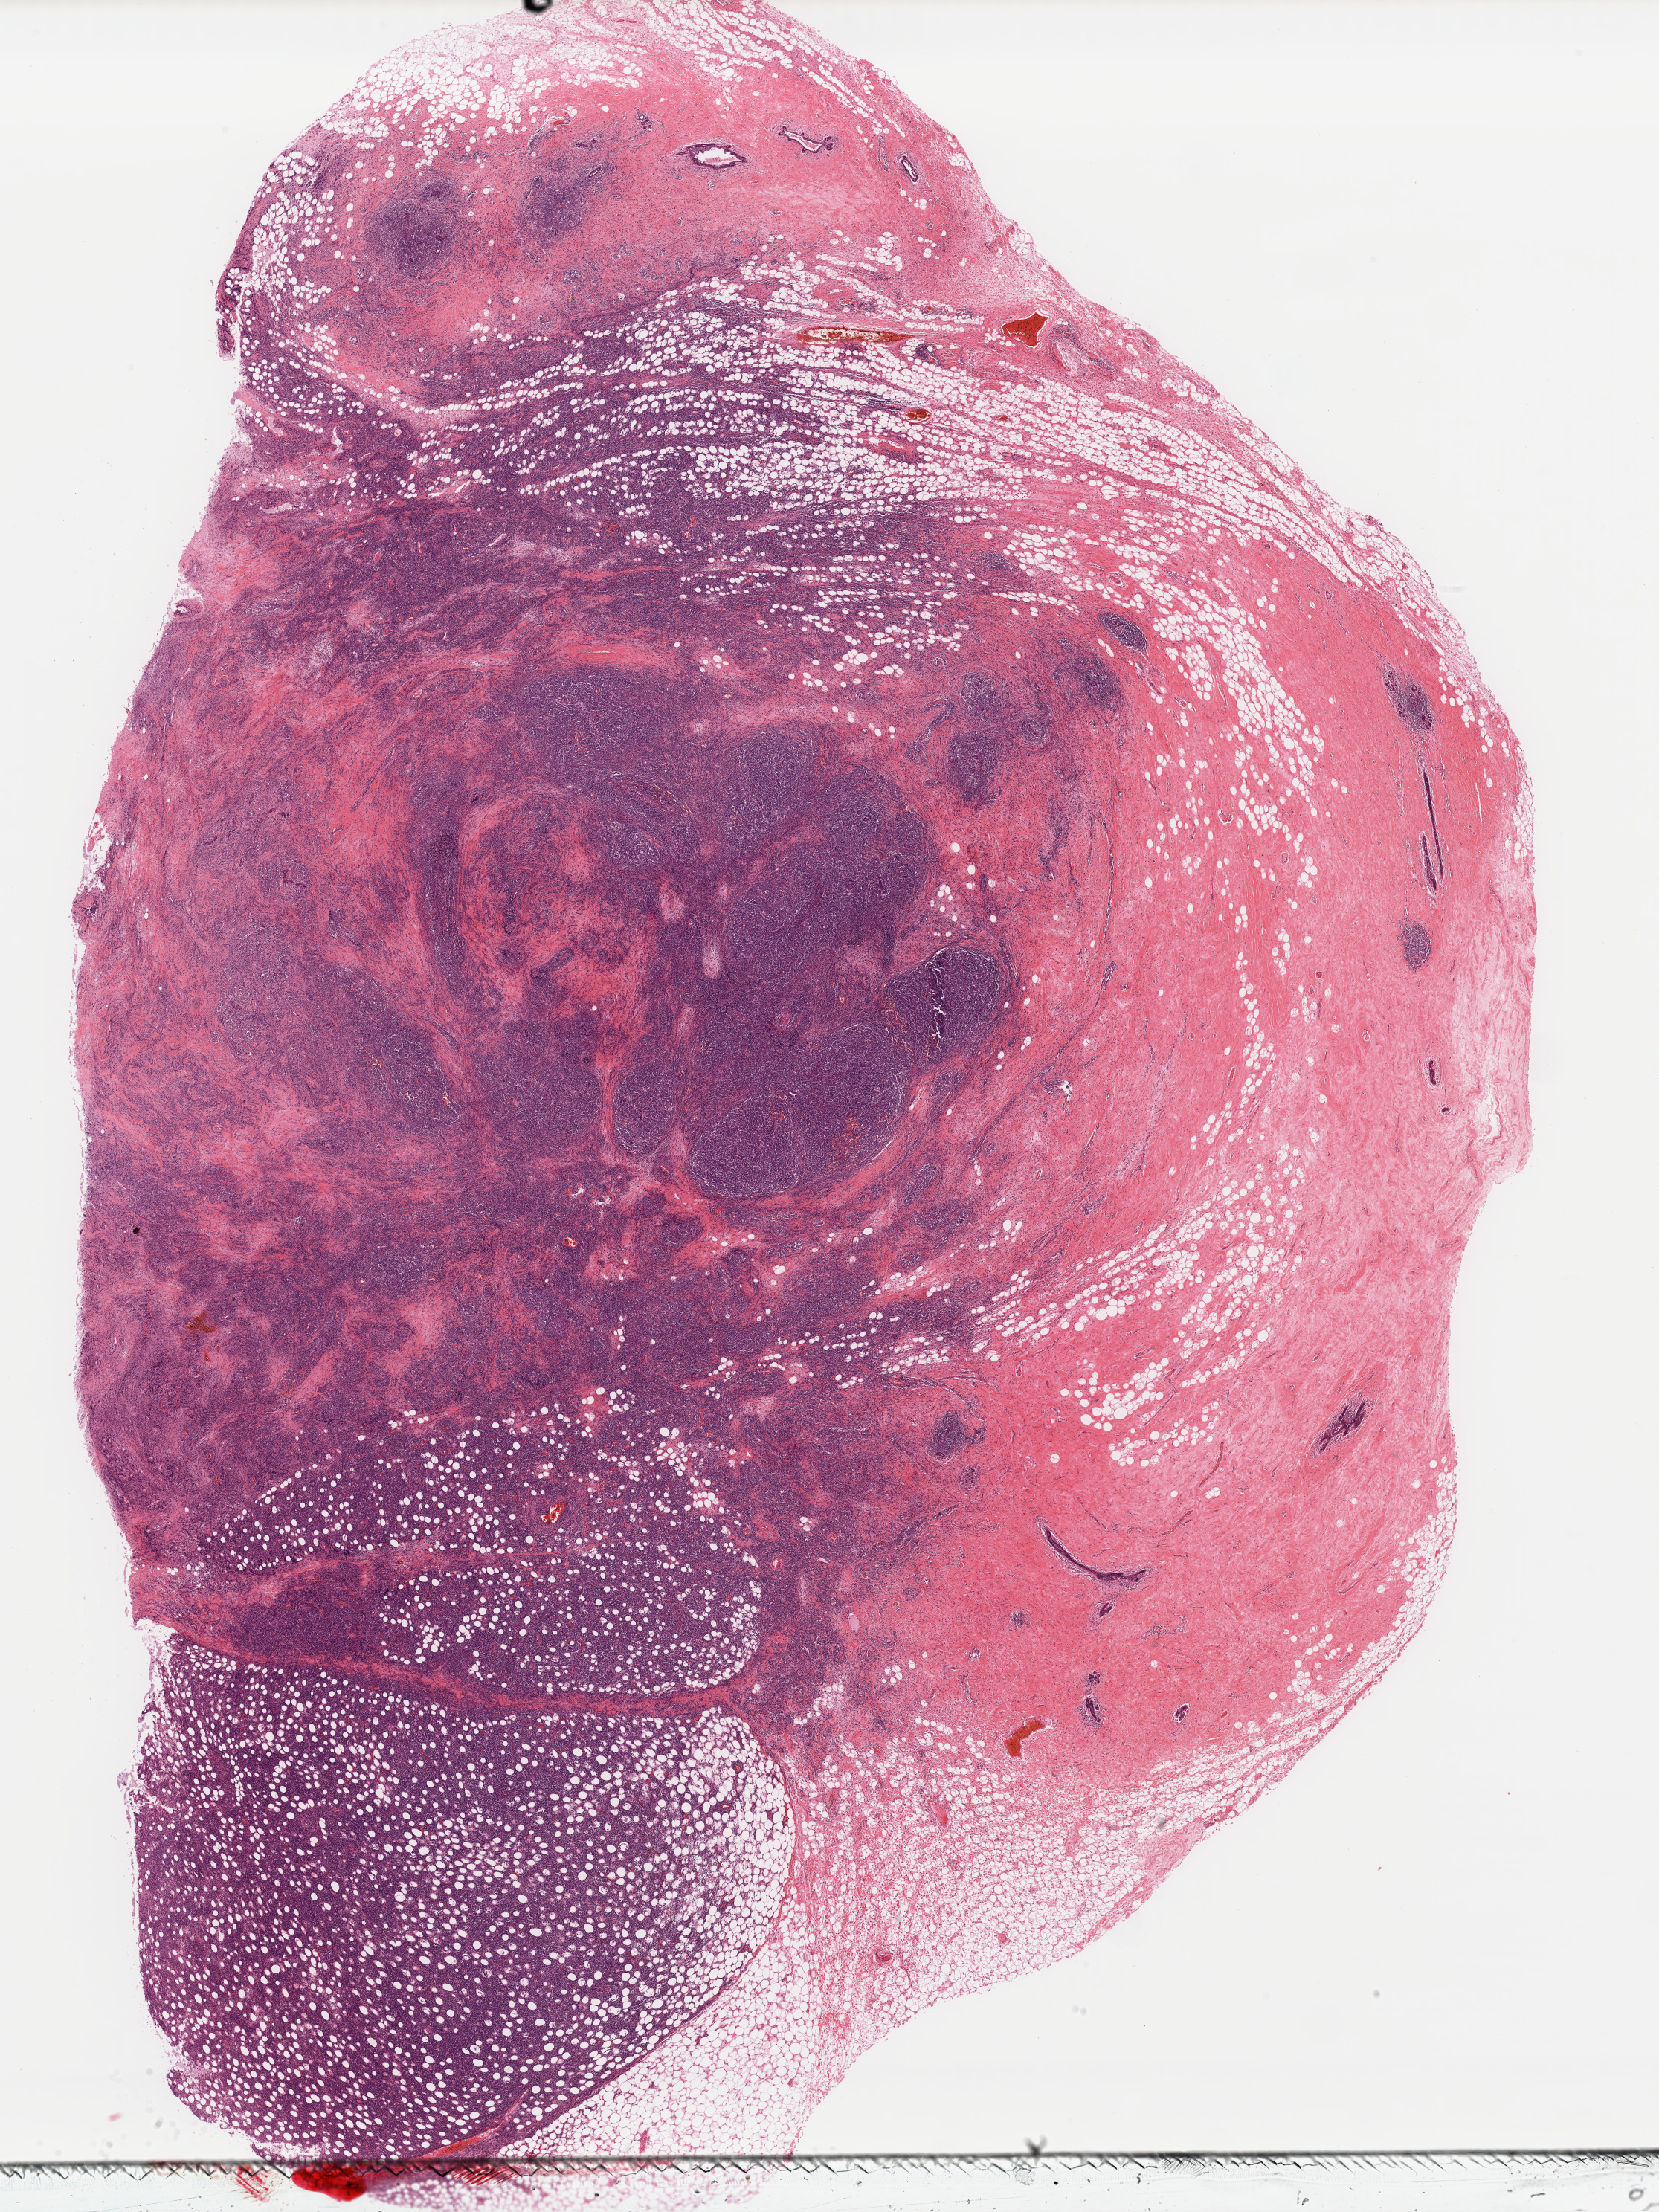
Digitized H&E tissue section (whole slide) — shown as a low-resolution overview of the whole scanned area (about 17.6 x 23.5 mm, acquisition: 40x scan), formalin-fixed paraffin-embedded (FFPE) diagnostic section, sample: primary tumour, lymphoid tissue. Female, age 54 years at initial diagnosis.
* histologic diagnosis: Diffuse large B-cell lymphoma, NOS (breast, NOS)